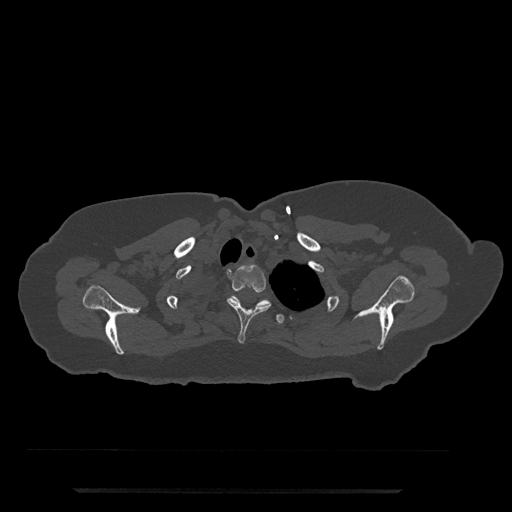
CT including the spine, one axial slice. Reconstruction kernel Br40s/3. 120 kVp. Bone window (W 1800 / L 400 HU). 512 × 512 image matrix, field of view 440 × 440 mm. Female patient, age 51 years. From the clinical record (not read from this slice): primary cancer: neuro.
Outlined on this slice (semi-automatic segmentation, software-assisted and operator-edited):
- T2 vertebra: box from (x=227, y=265) to (x=271, y=343) px
- T3 vertebra: (x=231, y=295)–(x=293, y=325)